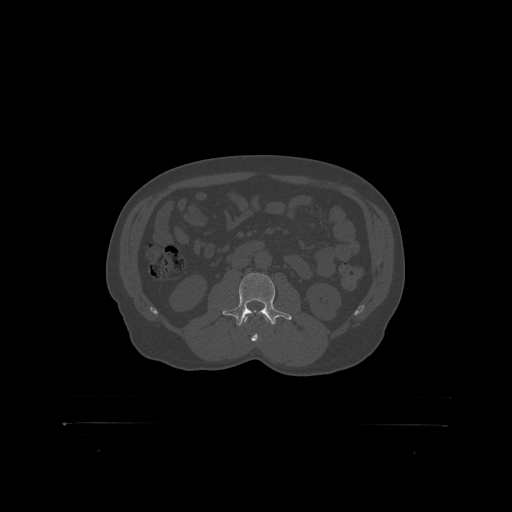
CT including the spine, one axial slice; slice 272 of 399 in the series (ordered by position); reconstruction kernel STANDARD; bone window (W 1800 / L 400 HU); 1.25 mm slice thickness; 512 × 512 image matrix. Patient: male, 46 years. From the clinical record (not read from this slice): primary cancer: skin.
Structures marked on this image (semi-automatic segmentation, software-assisted and operator-edited):
- L2 vertebra: bounding box (x1, y1, x2, y2) in pixels: (245, 316, 248, 319)
- L3 vertebra: (227, 273, 282, 319)